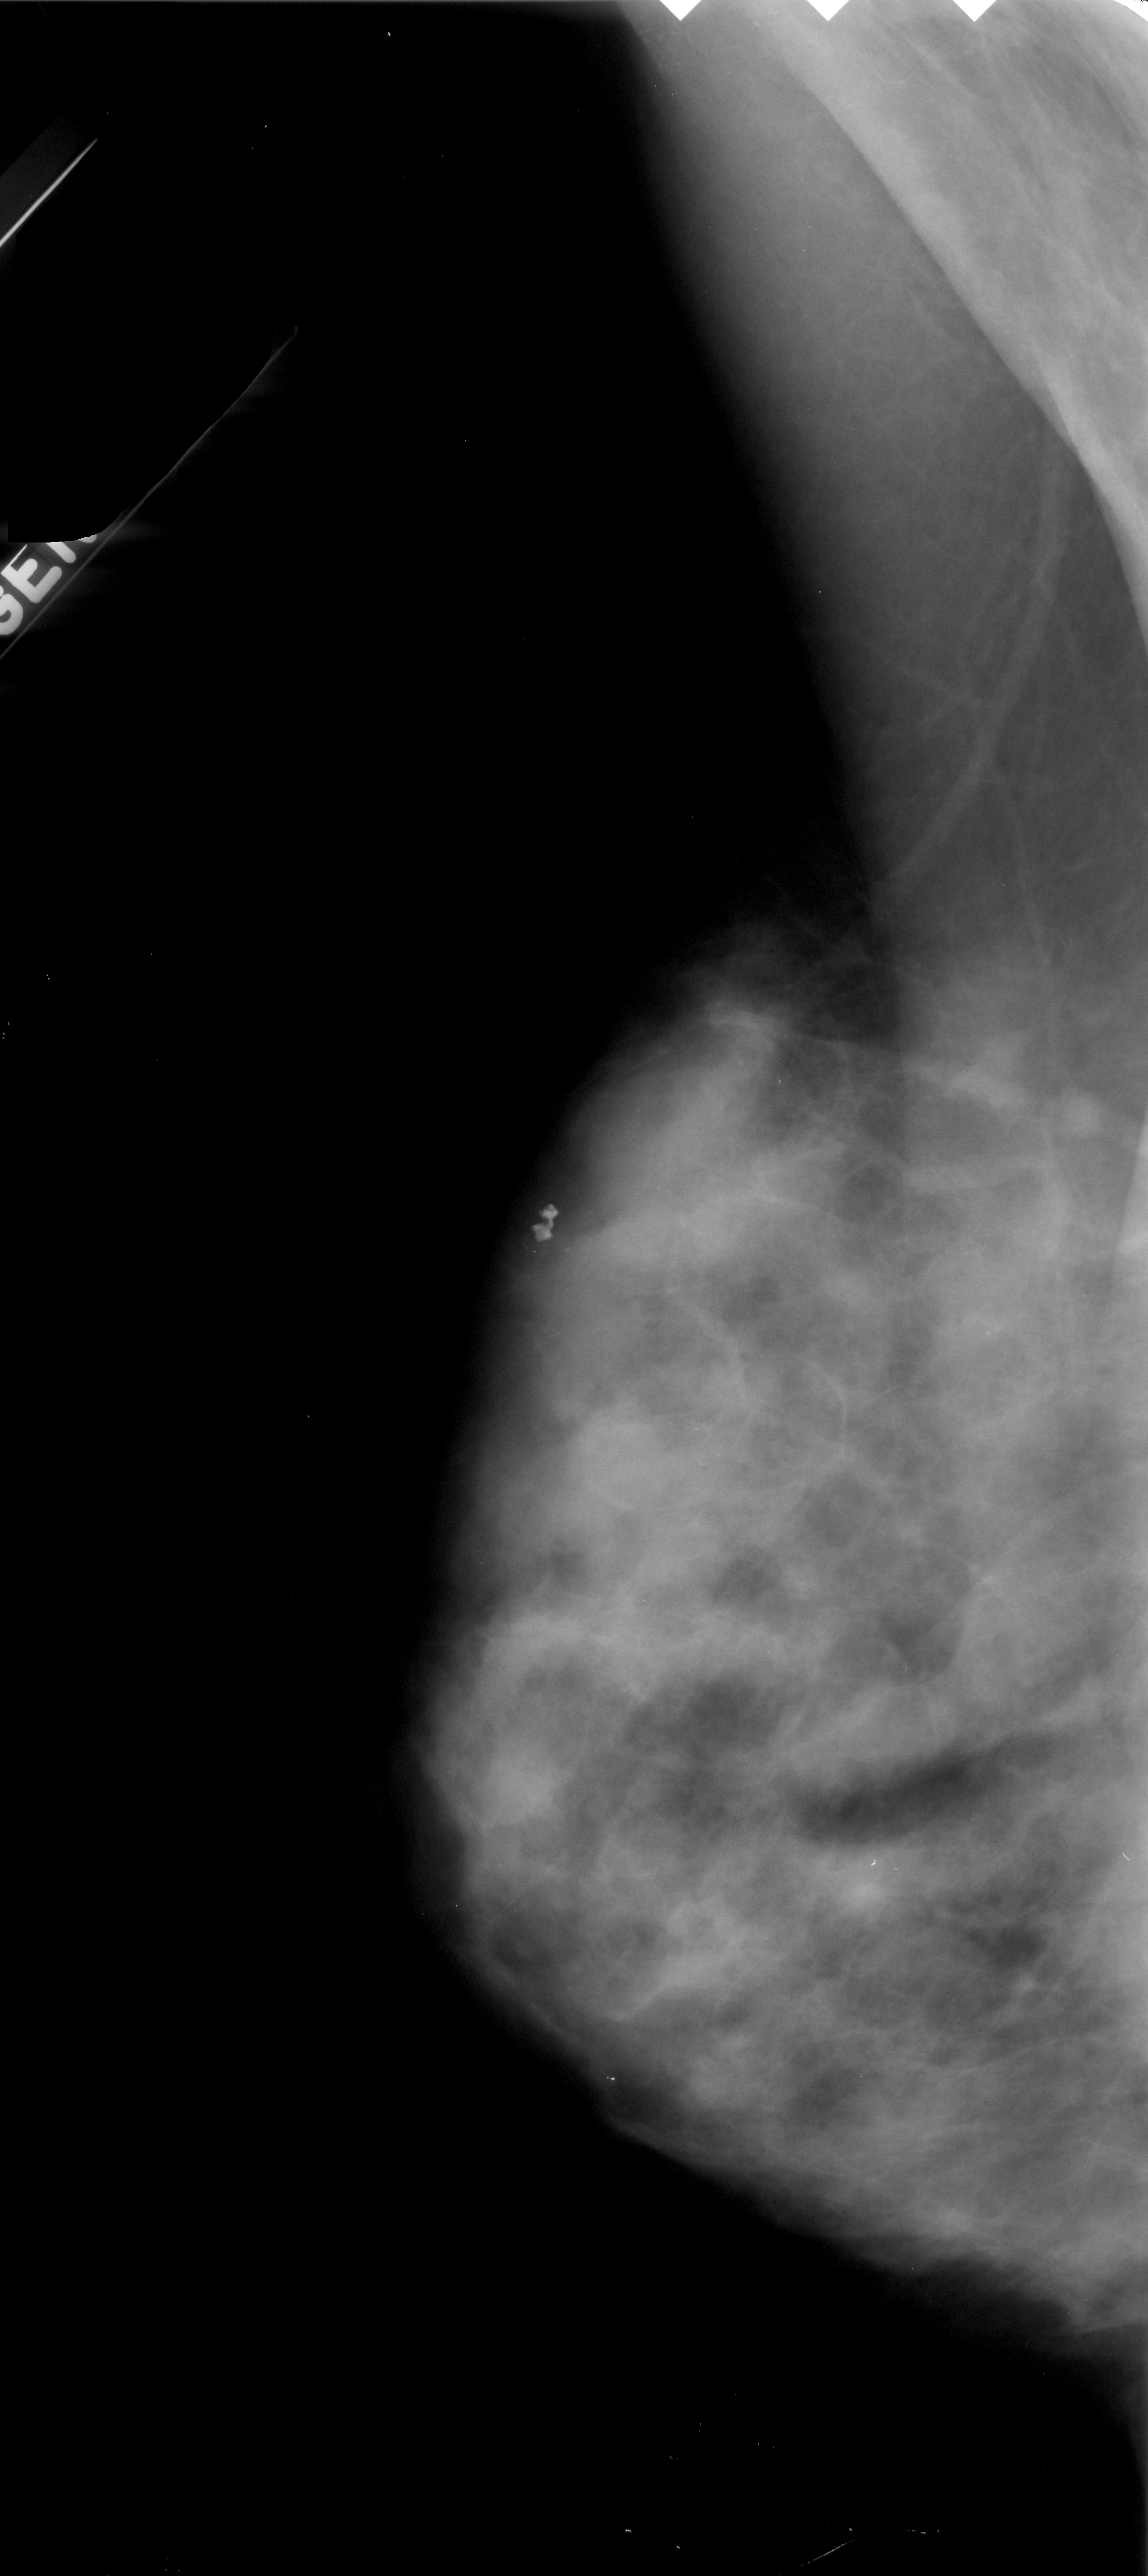
Scanned film-screen mammogram, left breast, MLO view.
Abnormality record for this image: calcifications, morphology pleomorphic, distribution clustered; BI-RADS assessment category 4; pathology (as recorded): malignant.